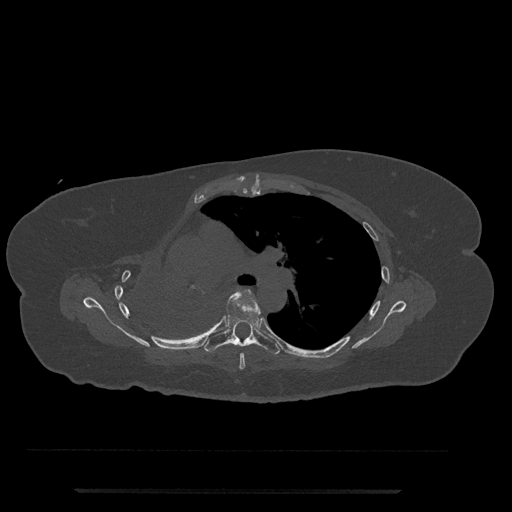
CT including the spine, one axial slice. Slice 509 of 797 in the series (ordered by position). Reconstruction kernel Br40s/3. Bone window (W 1800 / L 400 HU). 0.5 mm slice thickness. 512 × 512 image matrix, field of view 440 × 440 mm. Patient: female, 51 years. Case-level facts recorded for this patient, not image findings: primary cancer: neuro; vertebrae with lytic lesions (as recorded): T8.
Structures marked on this image (semi-automatic segmentation, software-assisted and operator-edited):
- T5 vertebra: bounding box <239,290,265,370> (left, top, right, bottom; pixels)
- T6 vertebra: <204,295,281,355>